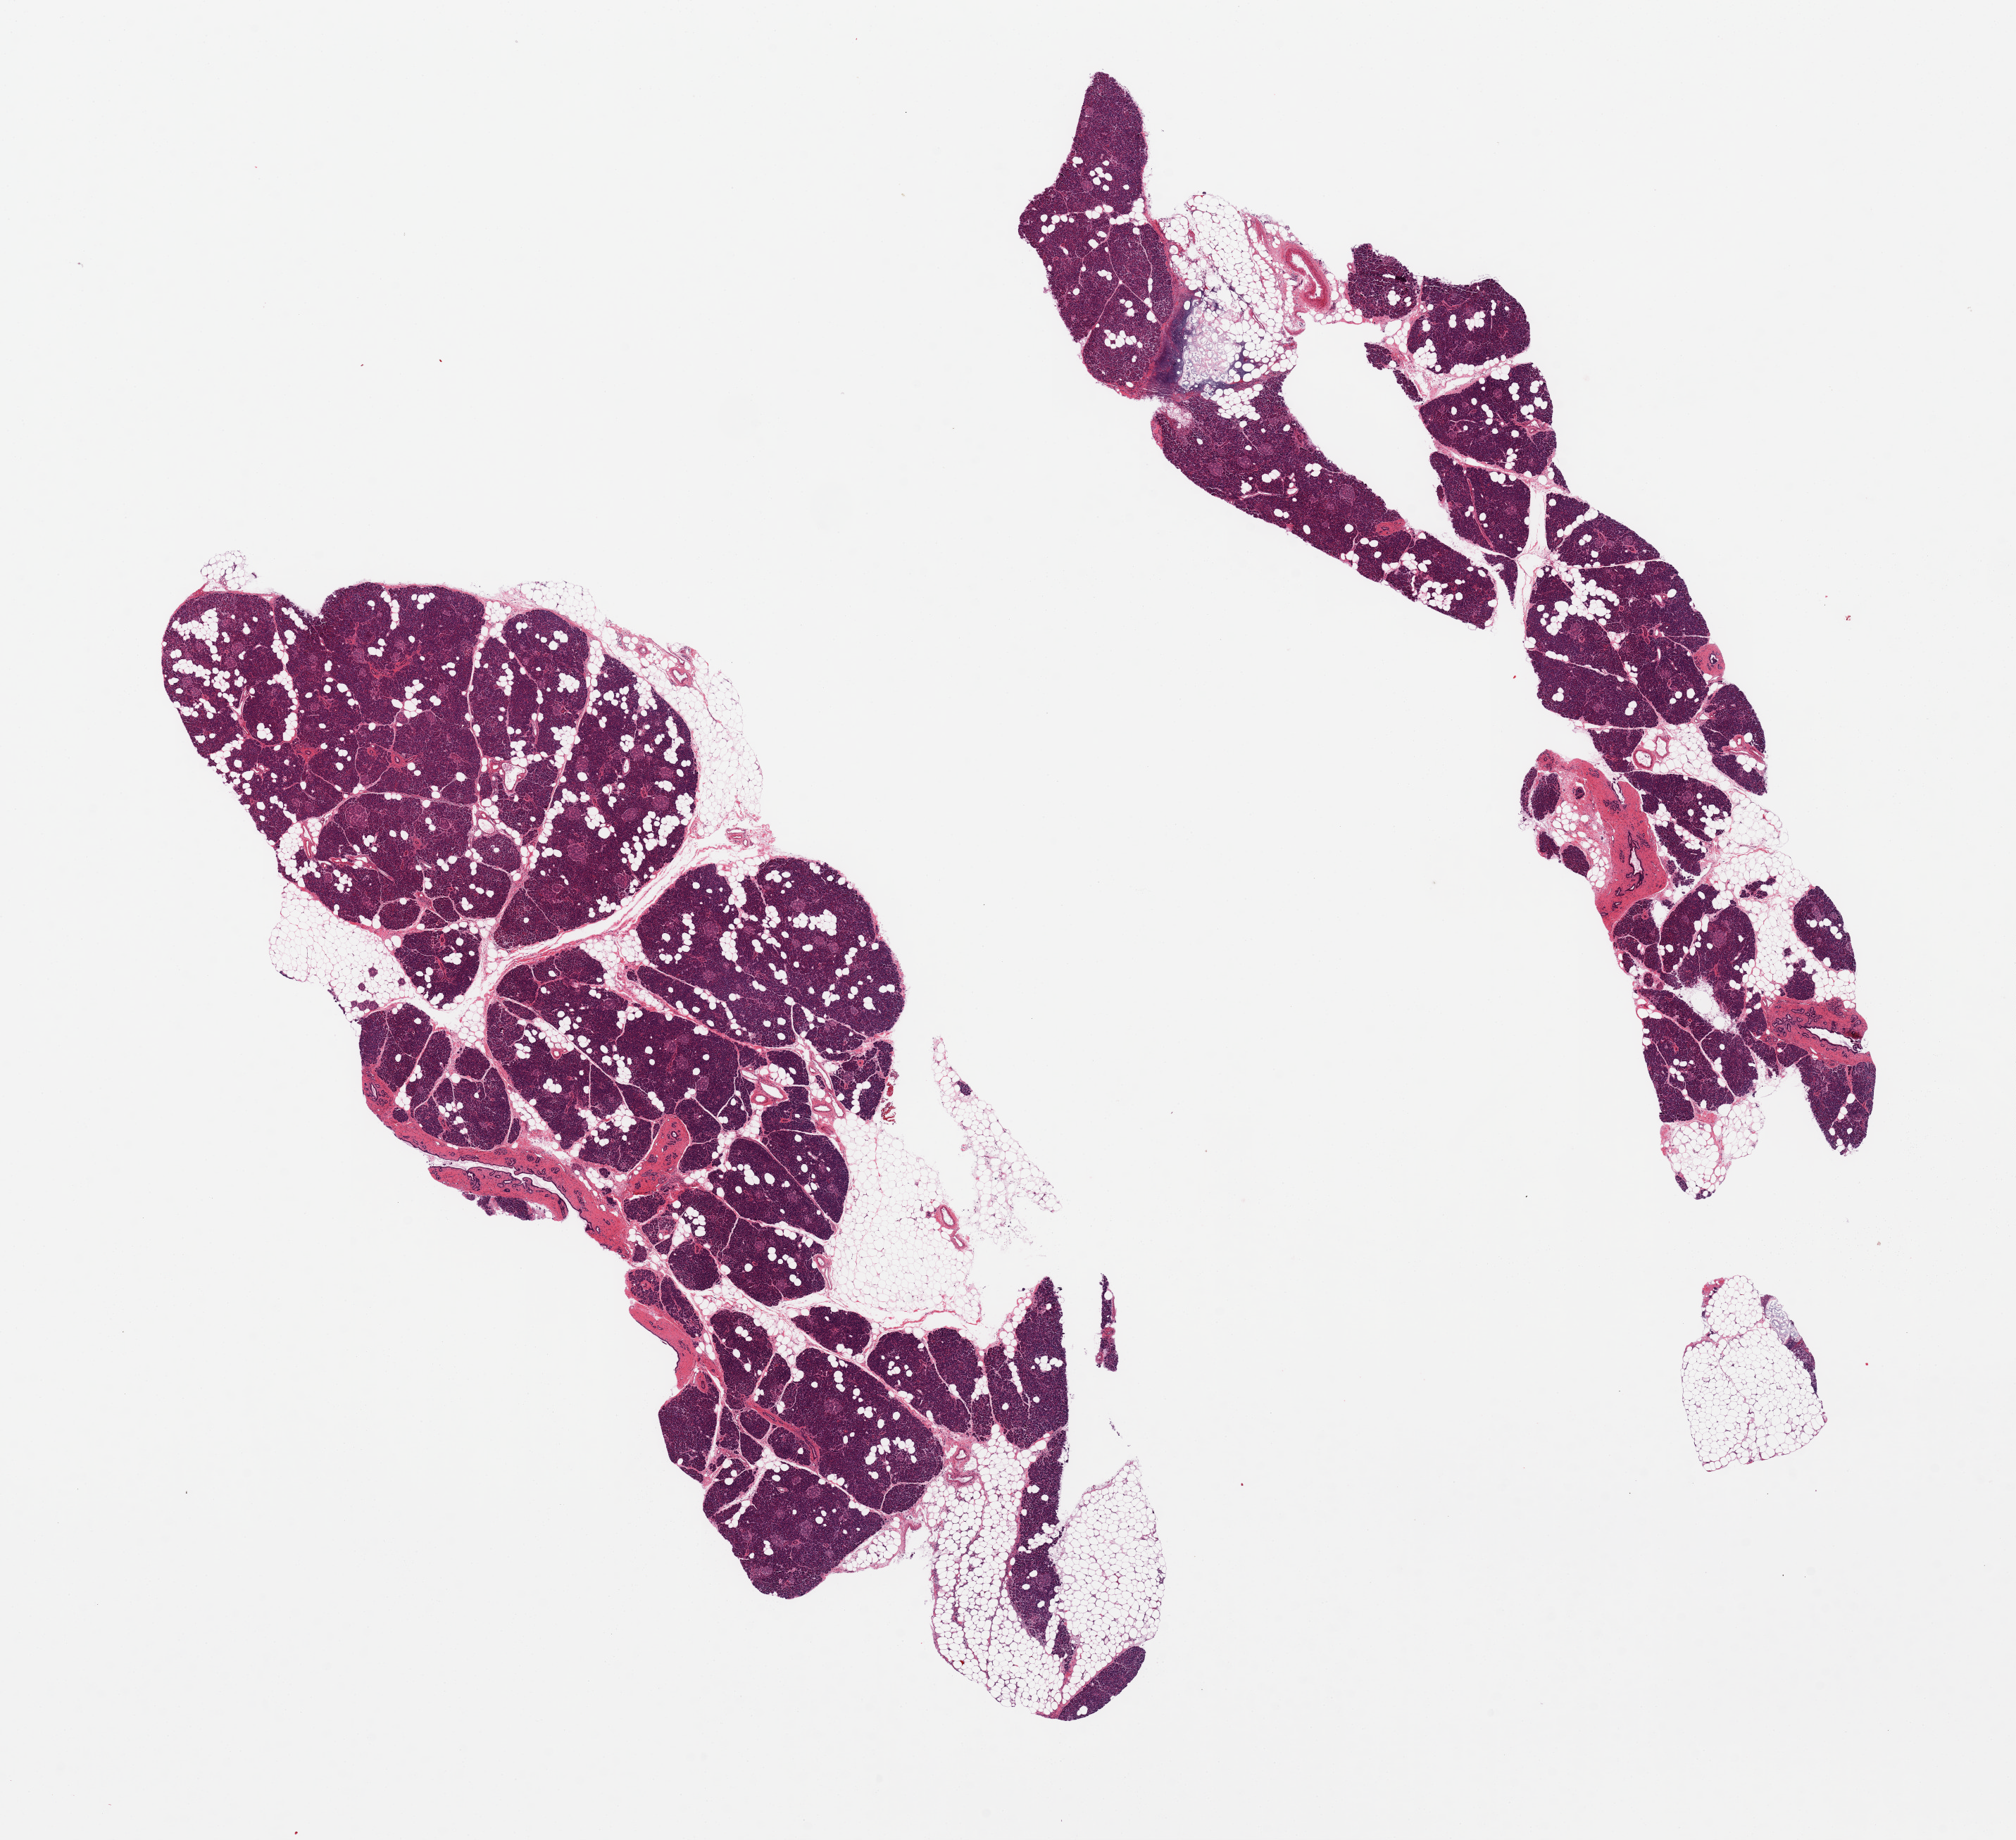
Hematoxylin and eosin (H&E) whole-slide image, a low-resolution overview of the entire scanned area, about 22.6 x 20.7 mm, PAXgene-fixed paraffin-embedded (PFPE) section, sampled site (target tissue): pancreas, donor tissue sample.
• review note (as recorded): 2 pieces, generally well preserved; Islets well preserved; focus of early saponification